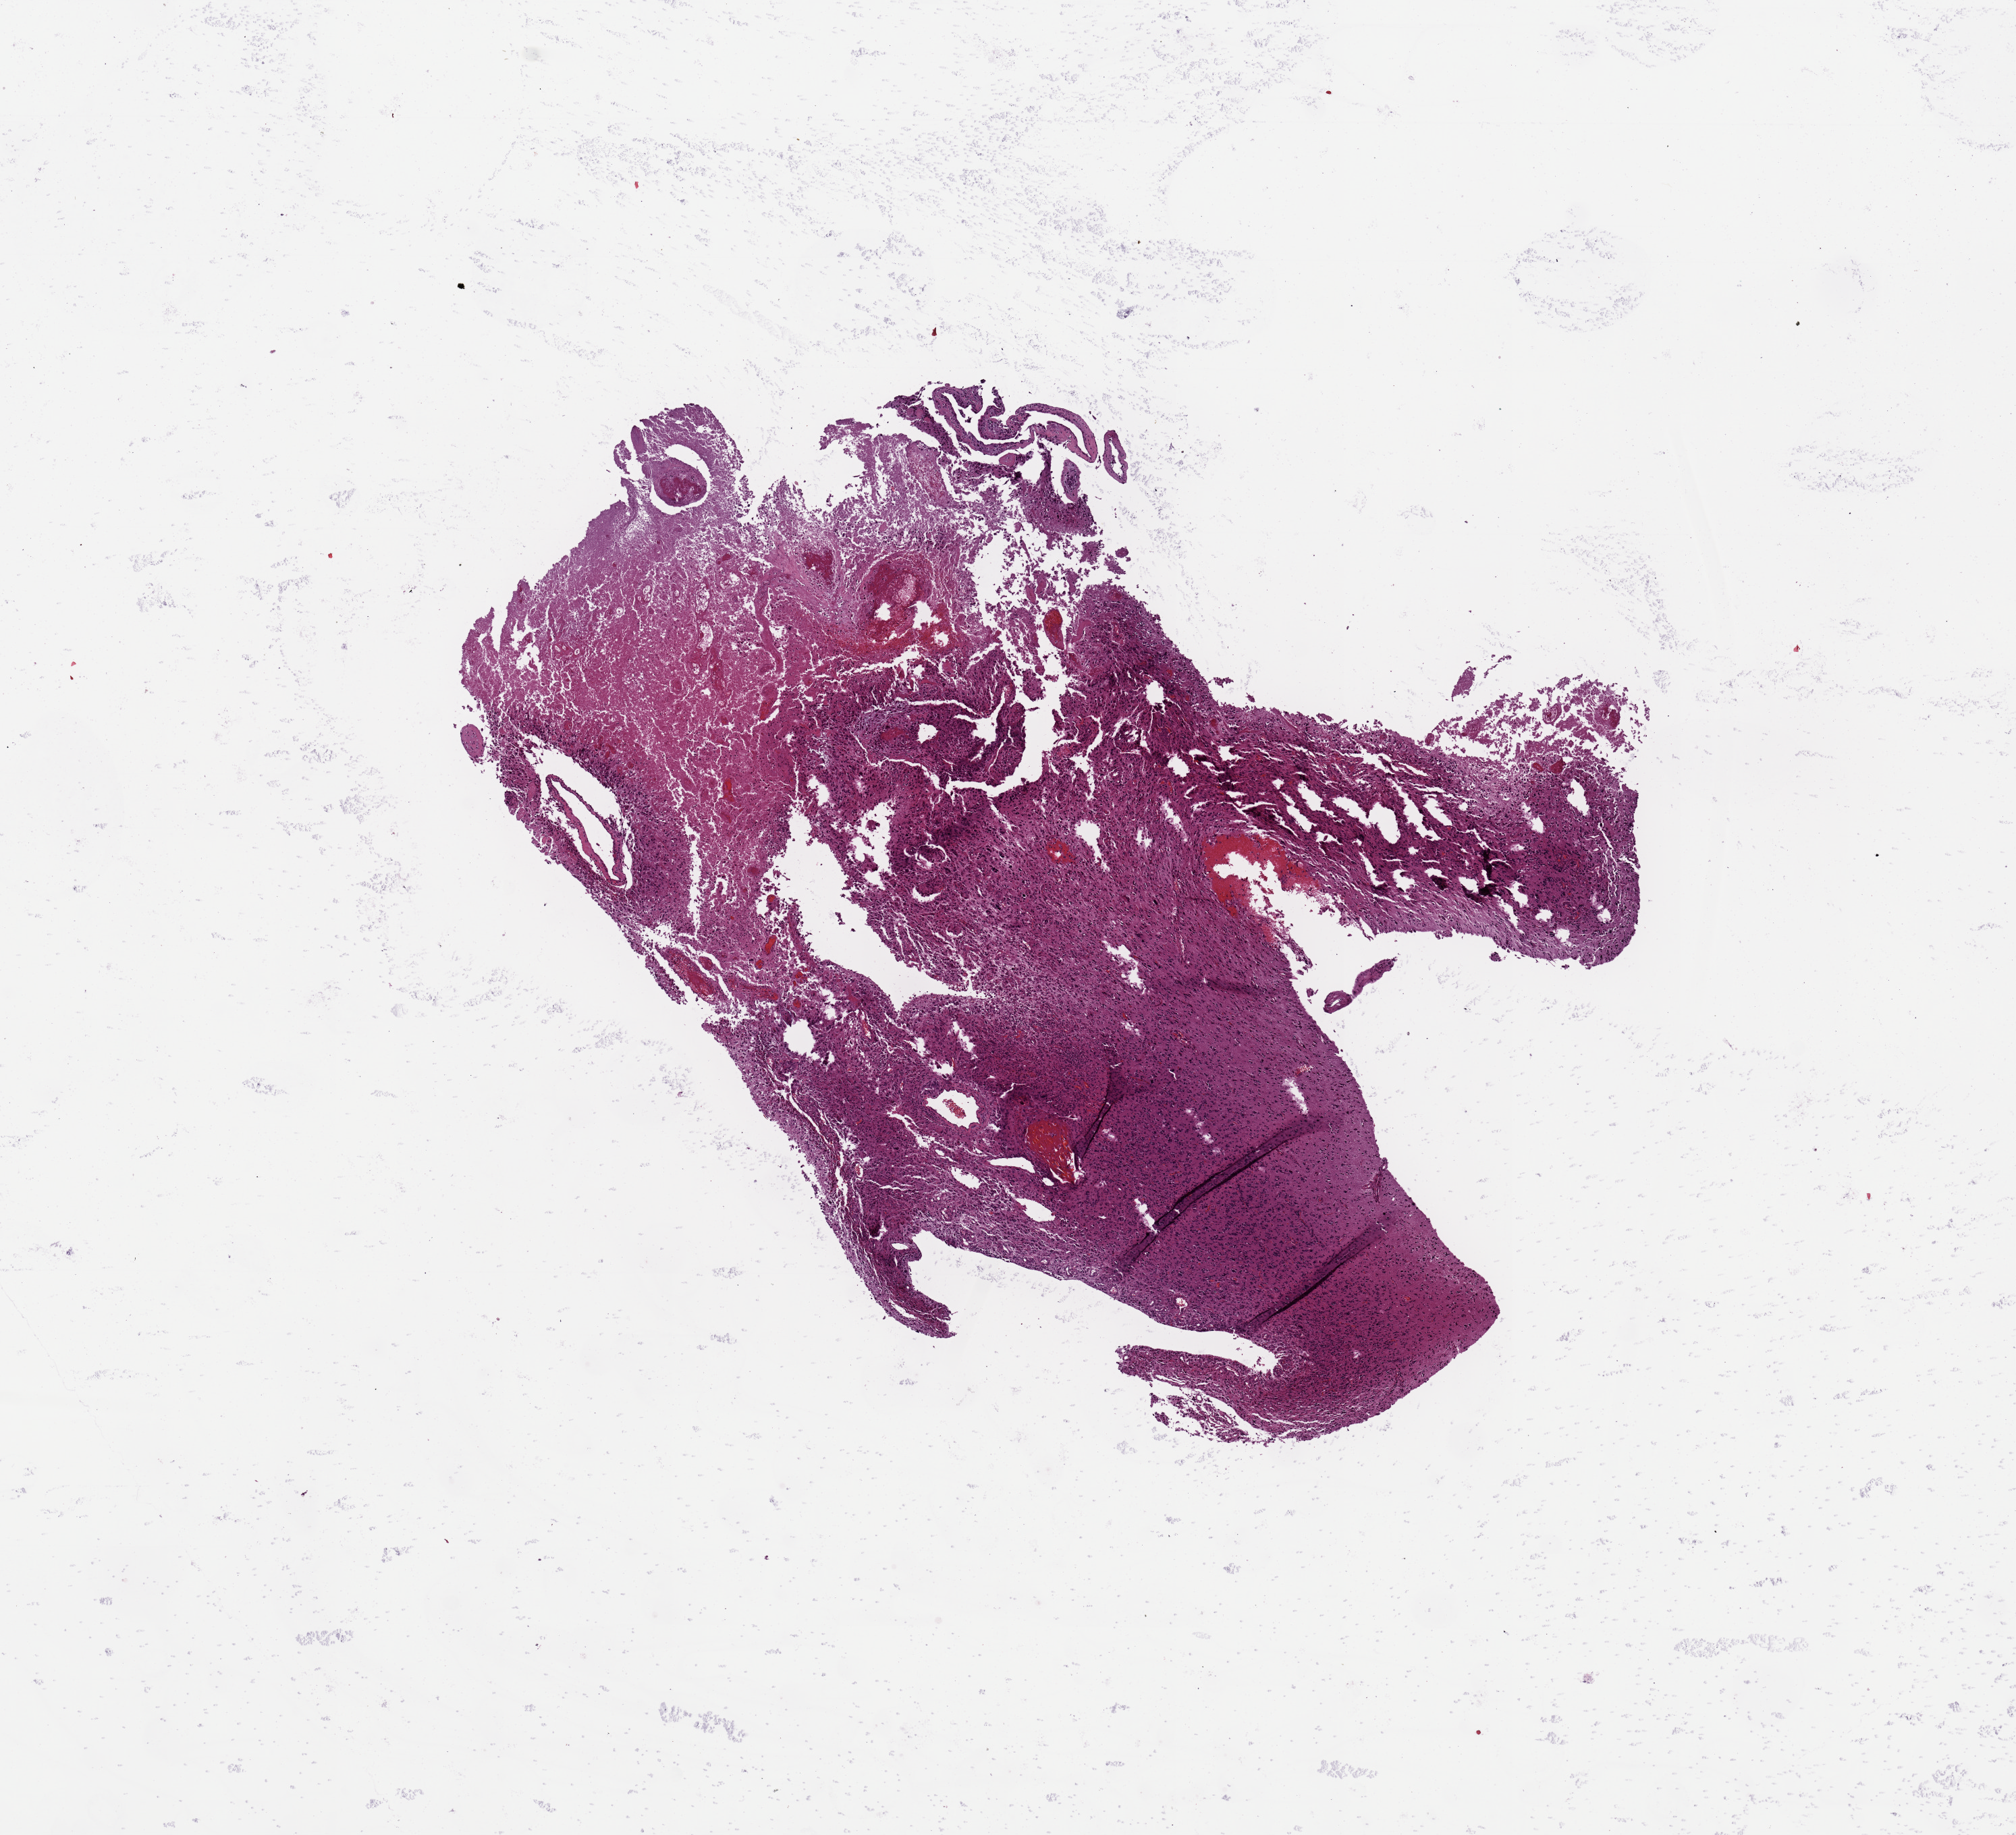
Whole-slide histology image, Hematoxylin and eosin (H&E) stained — low-resolution overview of the scanned area, about 11.8 x 10.8 mm. Brain, tumour tissue. Male, 64 y/o.
Diagnosis: Glioblastoma. Primary tumour site (as recorded): temporal lobe.